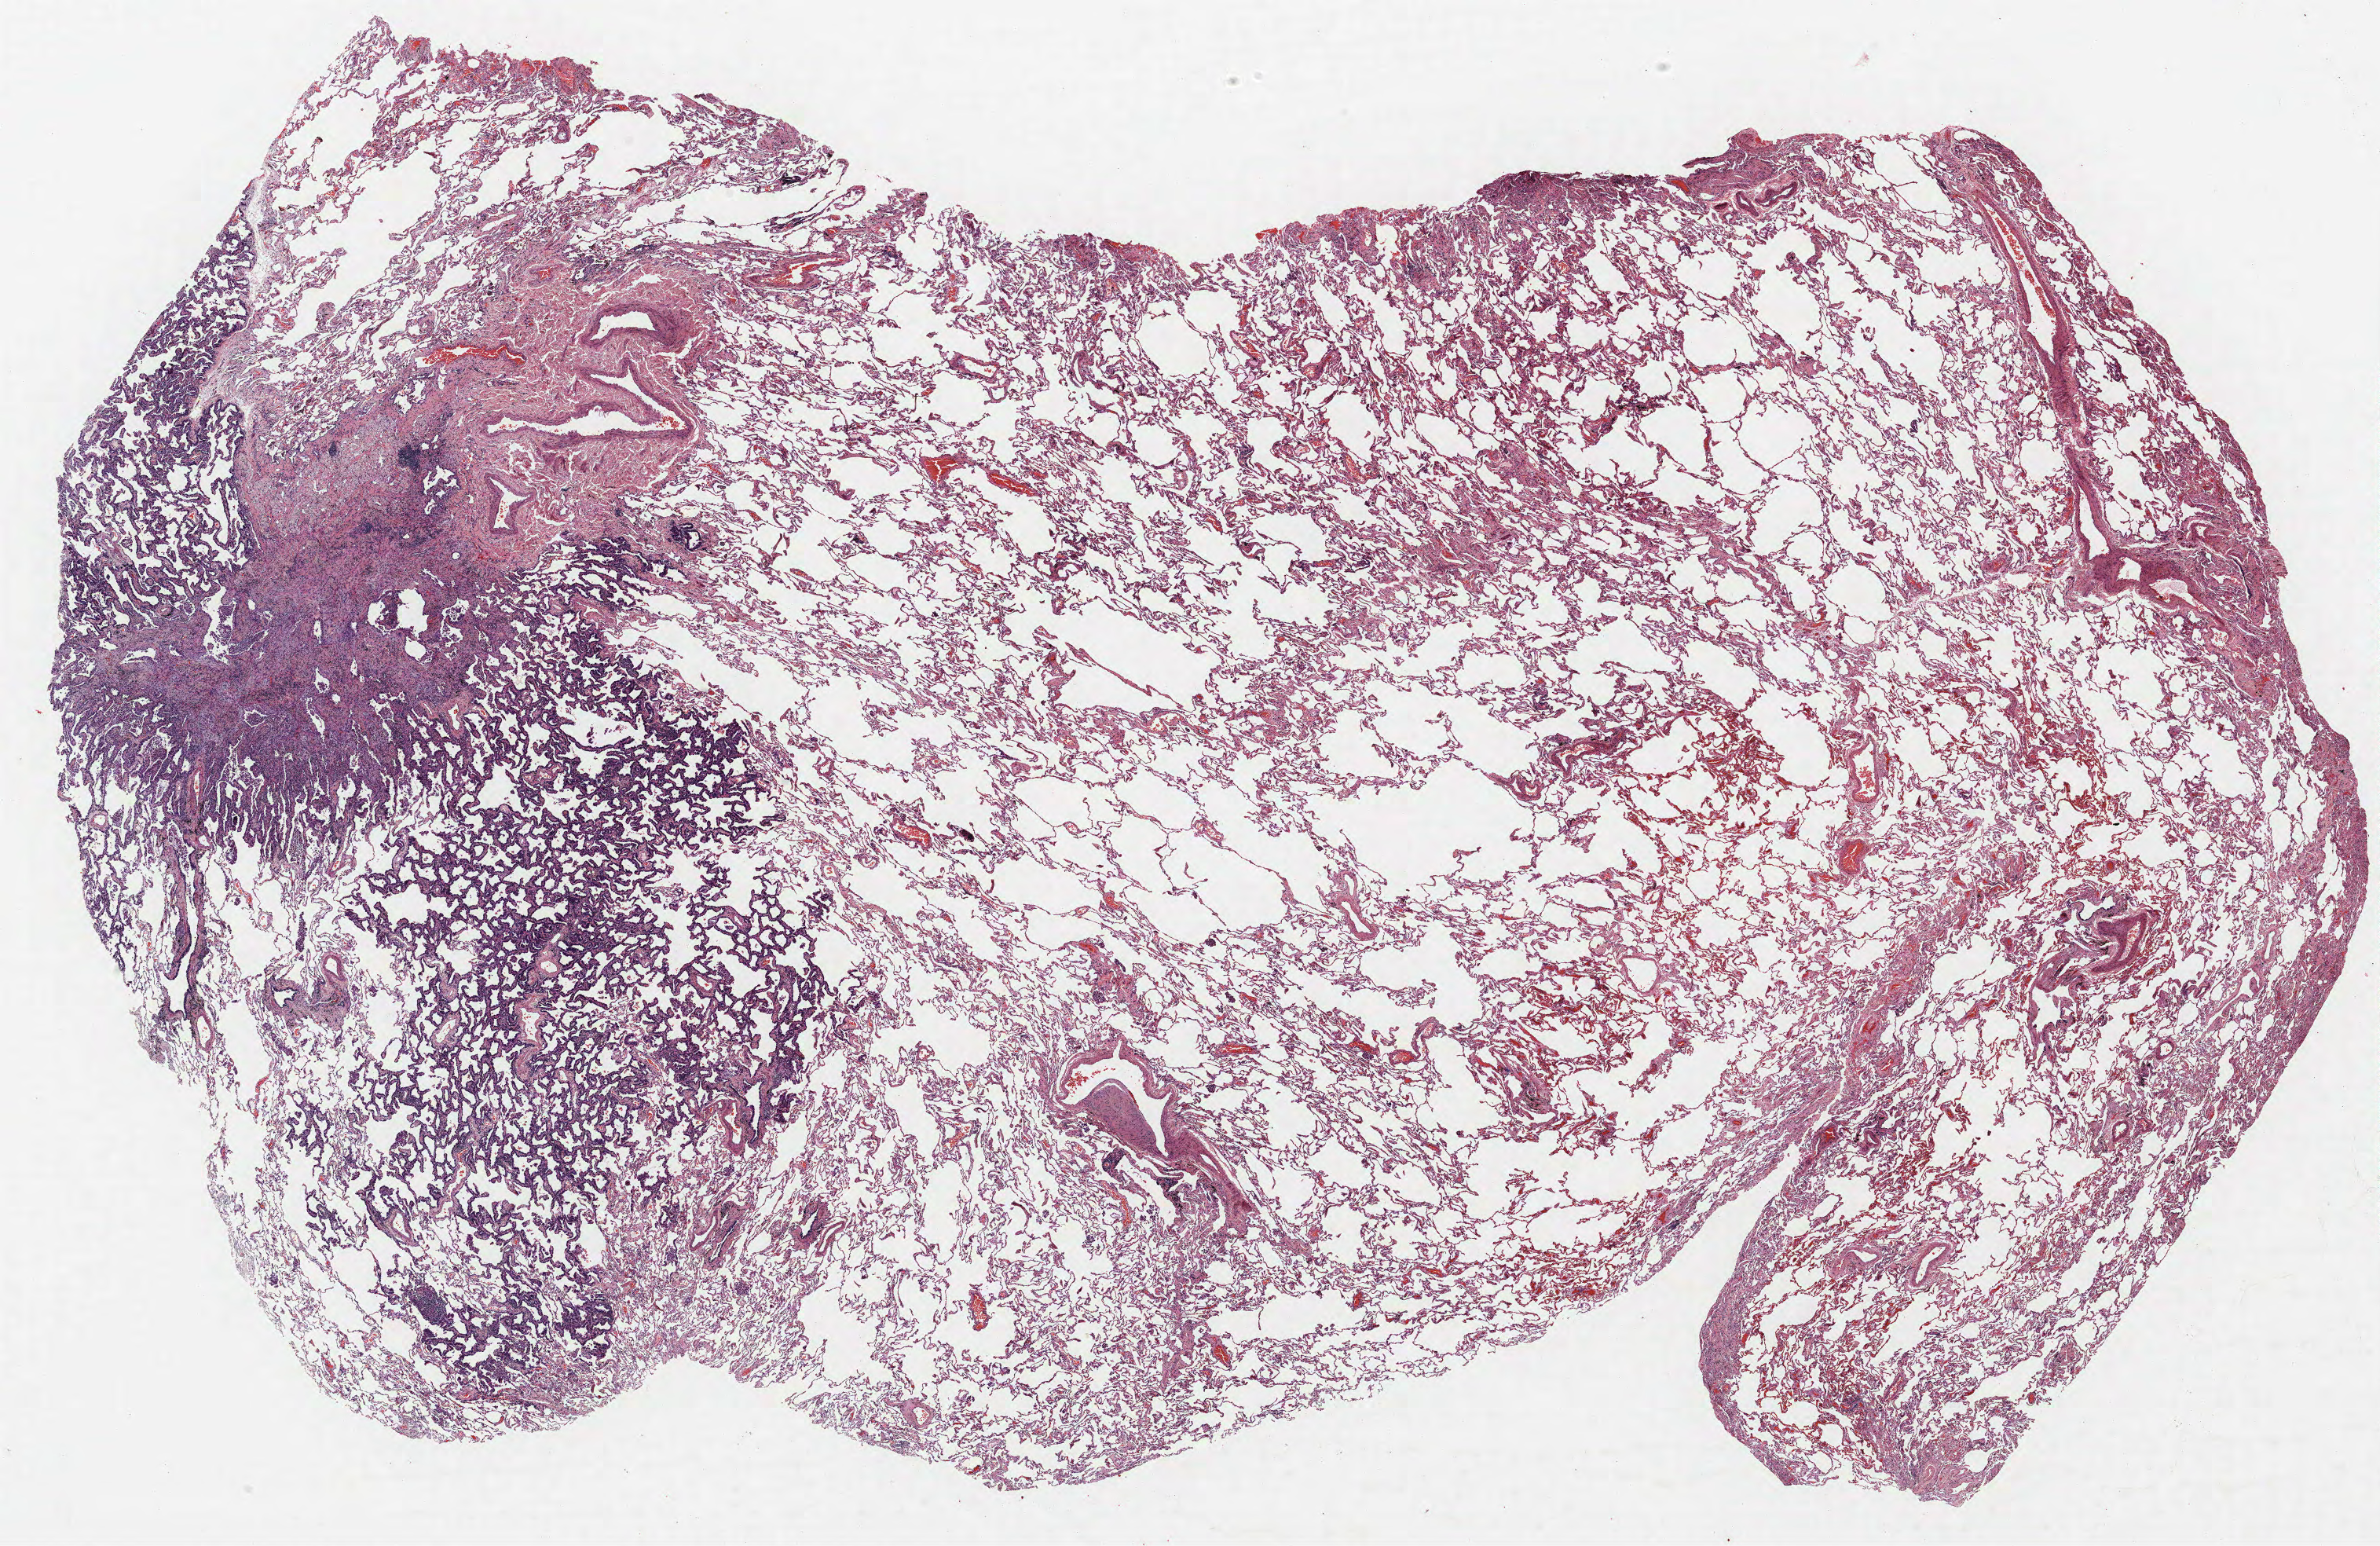
Hematoxylin and eosin (H&E) stained whole-slide image, whole scanned area (about 24.2 x 15.7 mm, from a 40x scan) shown as a low-resolution overview; formalin-fixed paraffin-embedded (FFPE) section; lung tissue. Female, age 56 at enrolment. Former smoker at enrolment.
Participant's lung-cancer diagnosis: Bronchiolo-alveolar carcinoma, non-mucinous.